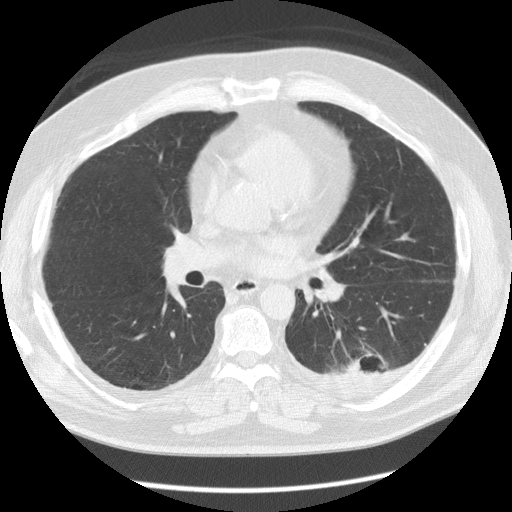
Axial slice from a low-dose chest CT screening exam; first (baseline) screen; lung window (W 1500 / L -600 HU); 512 × 512 image matrix, field of view 370 × 370 mm. Male, age 56 years at enrolment. Former smoker at enrolment.
Expert reader's lesion annotation, bounding box <324,341,396,393> (left, top, right, bottom; pixels). The screening reader recorded 4 non-calcified nodules or masses ≥4 mm on this exam (left lower lobe, left lower lobe, right middle lobe, left upper lobe); which of them this box marks is not recorded. Official screen result: positive, change unspecified: nodule(s) >= 4 mm or enlarging nodule(s), mass(es), or other non-specific abnormalities suspicious for lung cancer.